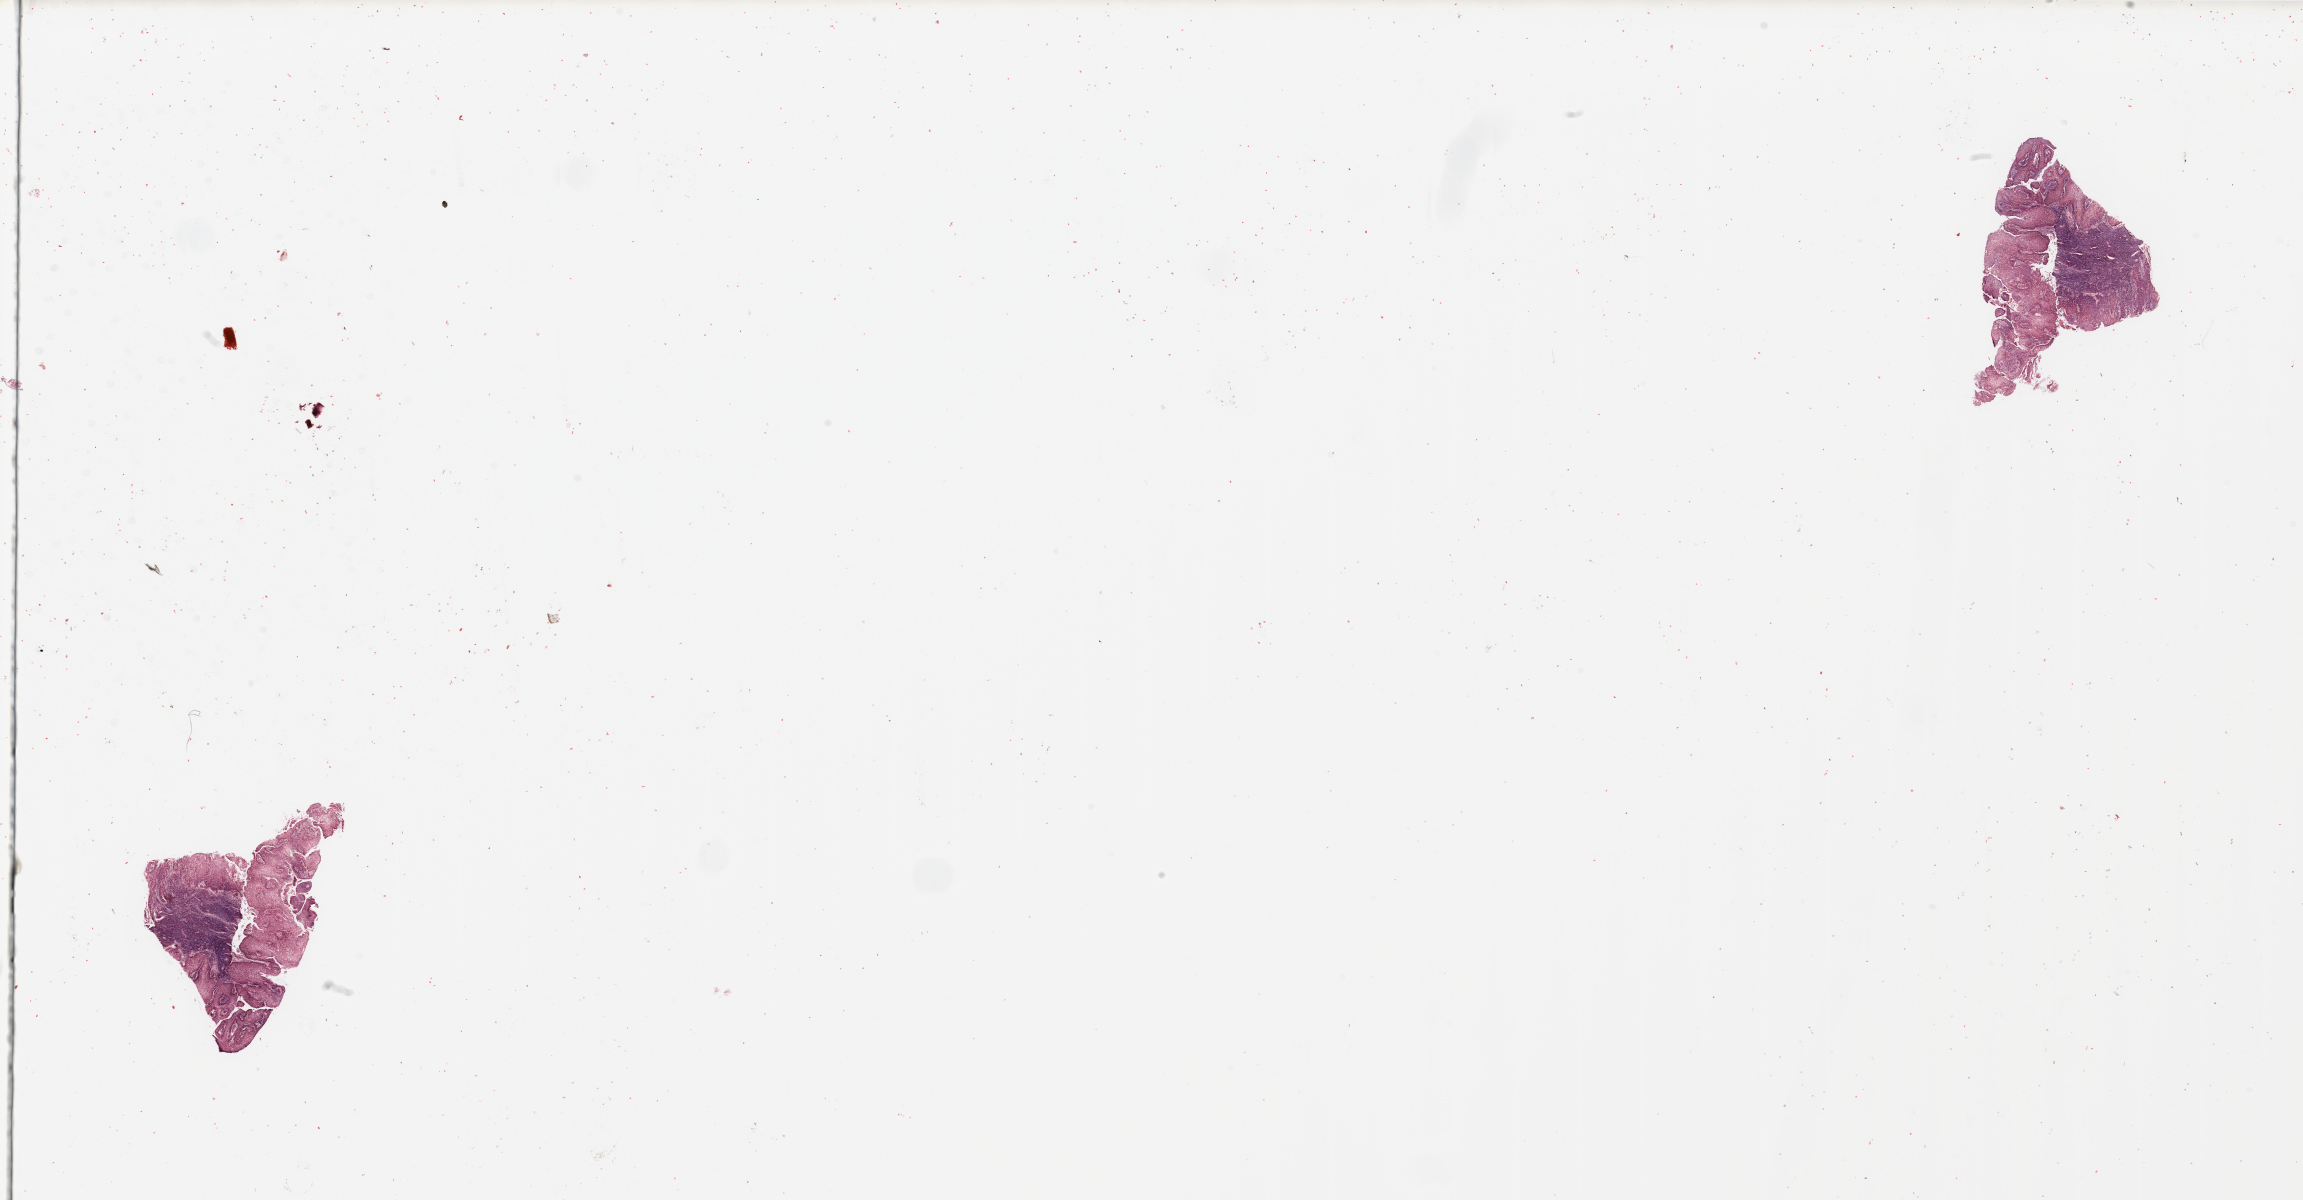
Whole-slide histology image, Hematoxylin and eosin (H&E) stained — shown as a low-resolution overview of the whole scanned area (about 36.4 x 19.0 mm). Head and neck, tissue type not recorded. 61-year-old male patient.
Patient diagnosis: Squamous cell carcinoma, NOS (larynx, NOS).